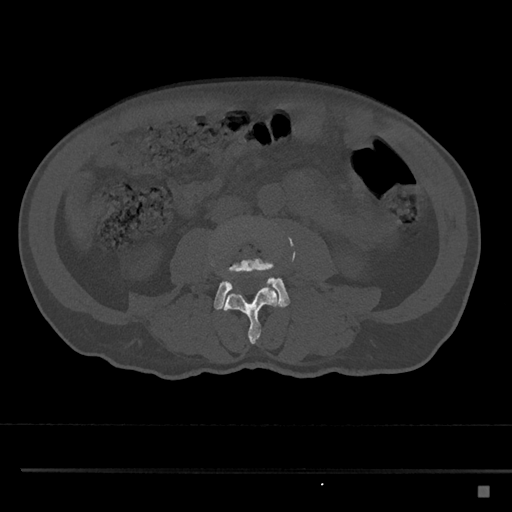
CT including the spine, one axial slice; slice 668 of 797 in the series (ordered by position); 120 kVp; bone window (W 1800 / L 400 HU); 0.5 mm slice thickness; 512 × 512 image matrix, field of view 391 × 391 mm. Male patient, age 59 years. From the clinical record (not read from this slice): primary cancer: prostate.
Outlined on this slice (semi-automatic segmentation, software-assisted and operator-edited):
- L3 vertebra: box from (x=211, y=234) to (x=280, y=344) px
- L4 vertebra: (x=213, y=251)–(x=290, y=310)